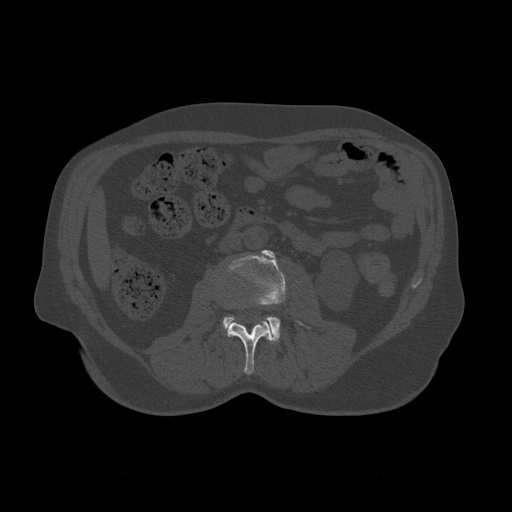
CT including the spine, one axial slice. Slice 319 of 450 in the series (ordered by position). 120 kVp. Bone window (W 1800 / L 400 HU). 512 × 512 image matrix, field of view 405 × 405 mm. Patient age 75 years. From the clinical record (not read from this slice): primary cancer: prostate.
Outlined on this slice (semi-automatic segmentation, software-assisted and operator-edited):
- L2 vertebra: bounding box (x1, y1, x2, y2) in pixels: (225, 304, 274, 375)
- L3 vertebra: (223, 250, 310, 344)